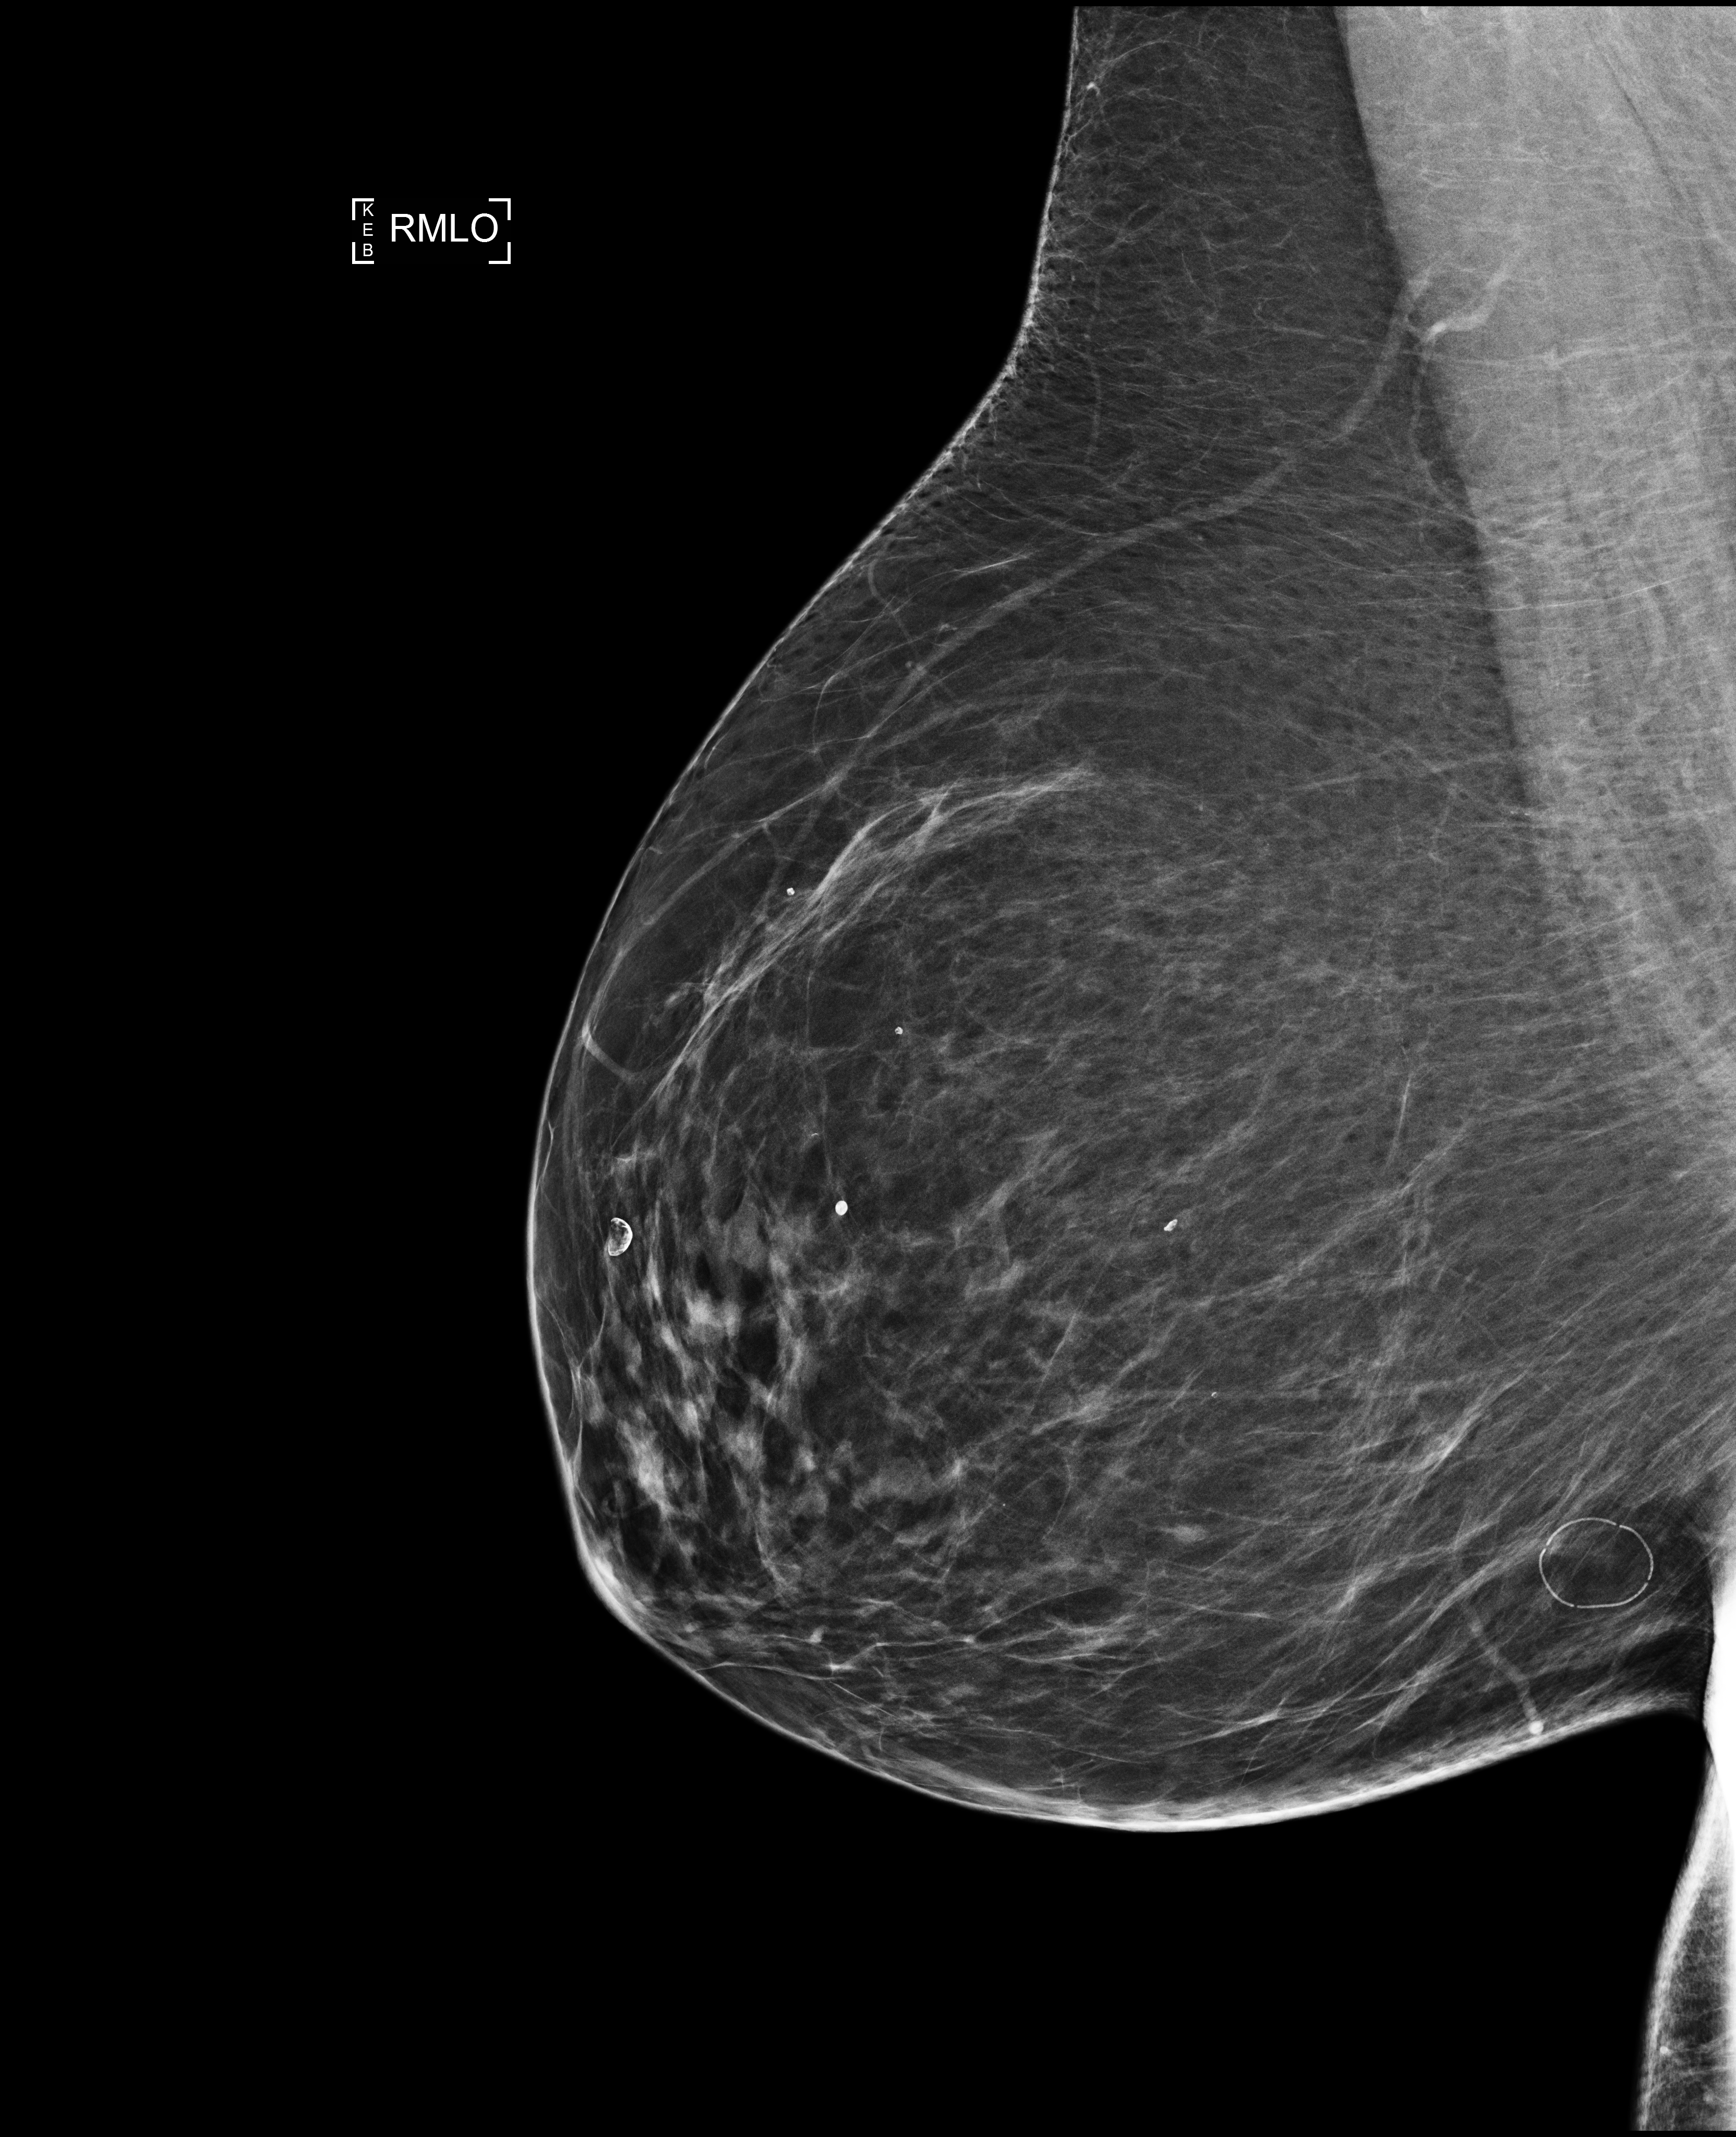
Screening examination; system: Selenia Dimensions. Female patient, age 67 years.
Image type: full-field digital mammogram. Breast: right. Projection: medio-lateral oblique projection.